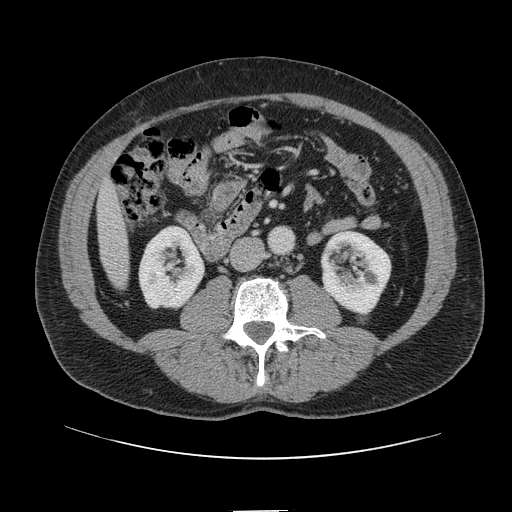
Contrast-enhanced abdominal CT, one axial slice; slice 17 of 161 in the series (ordered by position); intravenous contrast given; soft-tissue window (W 400 / L 40 HU); 2.5 mm slice thickness; 512 × 512 image matrix, field of view 412 × 412 mm. Male patient, age 66 years. Case-level facts recorded for this patient, not image findings: diagnosis: colorectal cancer liver metastases, imaged before liver resection; multiple liver metastases: no.
Structures marked on this image (outlined manually by an expert reader):
- liver: box from (x=98, y=183) to (x=129, y=288) px
- planned liver remnant (the part of the liver to remain after resection): (x=98, y=183)–(x=124, y=247)